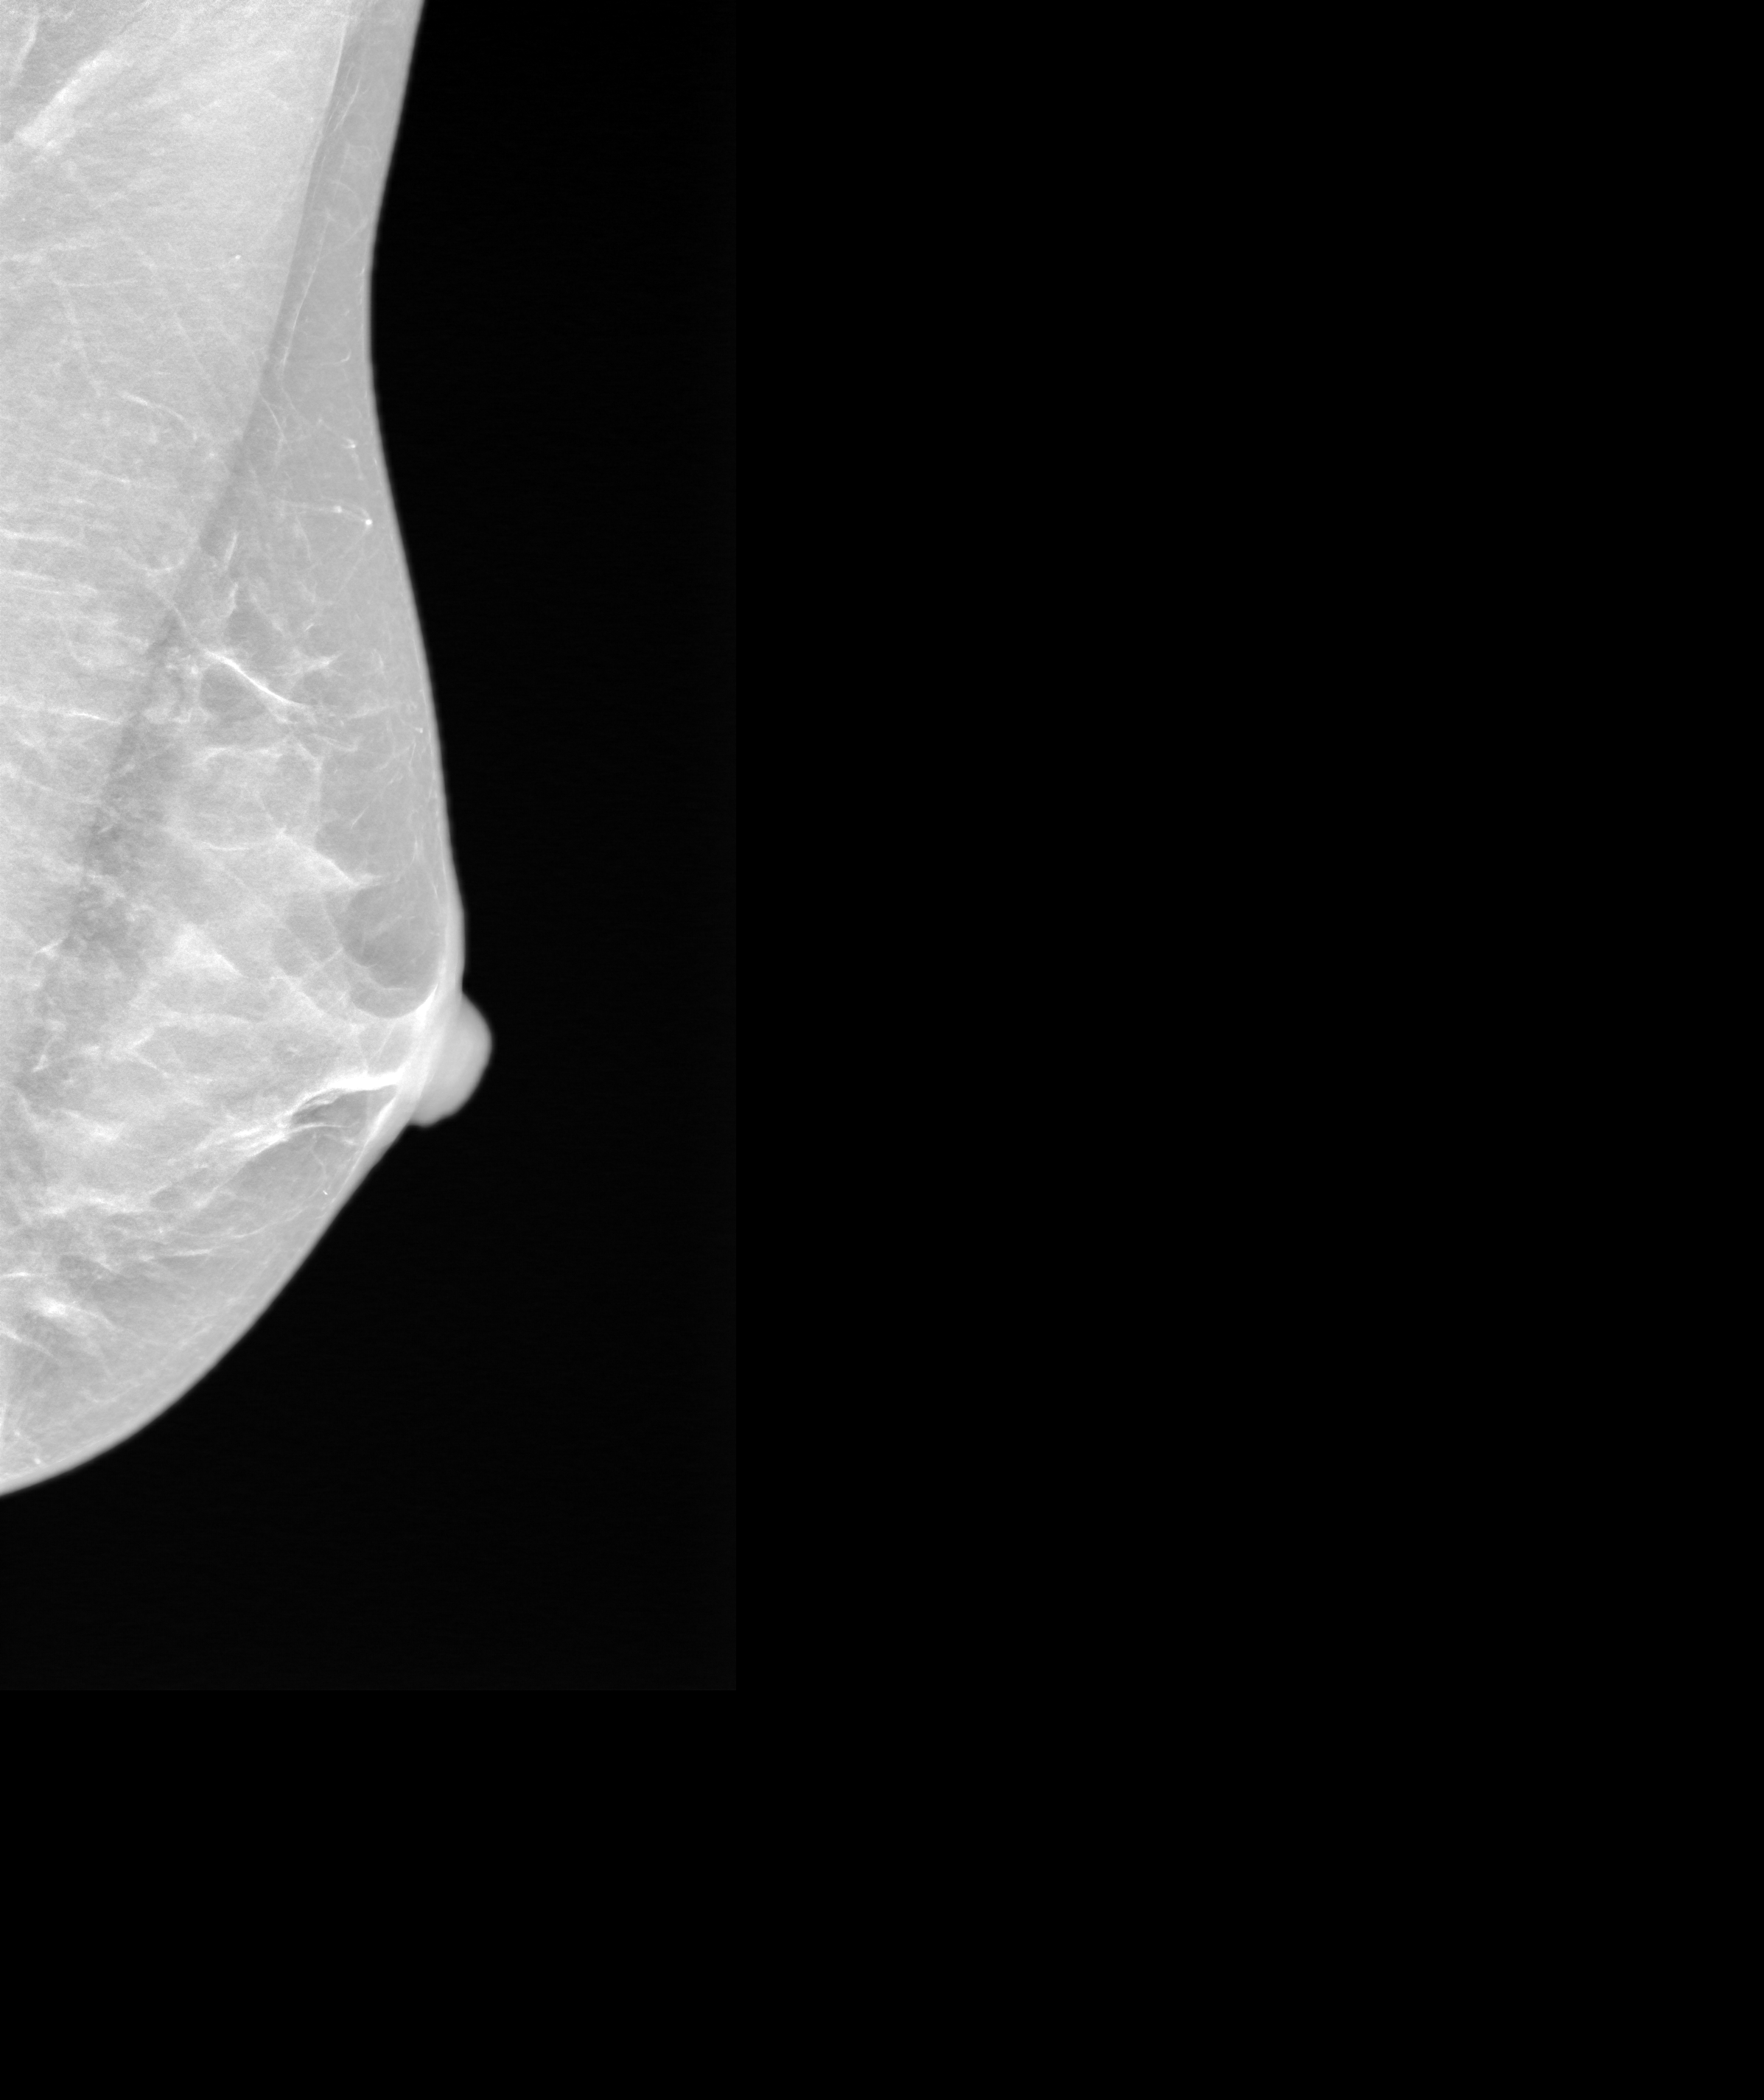
Screening examination; system: SenoIris_1SP2(440). Patient aged 47 years (female).
Image type: synthesized 2-D view from tomosynthesis. Breast: left. Projection: mediolateral oblique (MLO) view.